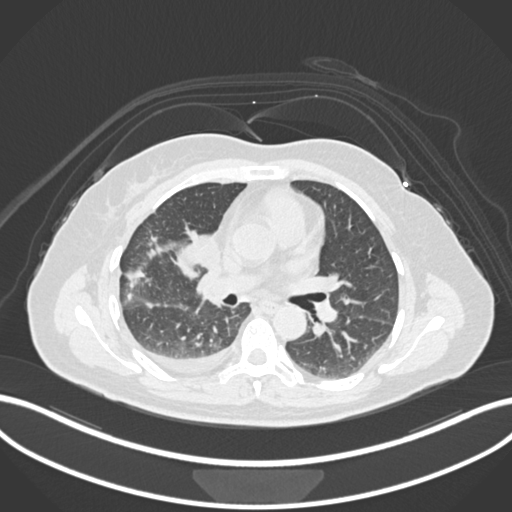
Chest CT, one axial slice. 120 kVp. Lung window (W 1500 / L -600 HU). 1 mm slice thickness. 512 × 512 image matrix, field of view 400 × 400 mm. Patient: female, 52 years. From the clinical record (not read from this slice): clinical TNM (as recorded): T3 N1 M1.
Structures marked on this image (bounding box drawn by a radiologist):
- lung tumour (recorded histology: adenocarcinoma): bounding box (x1, y1, x2, y2) in pixels: (175, 226, 219, 272)